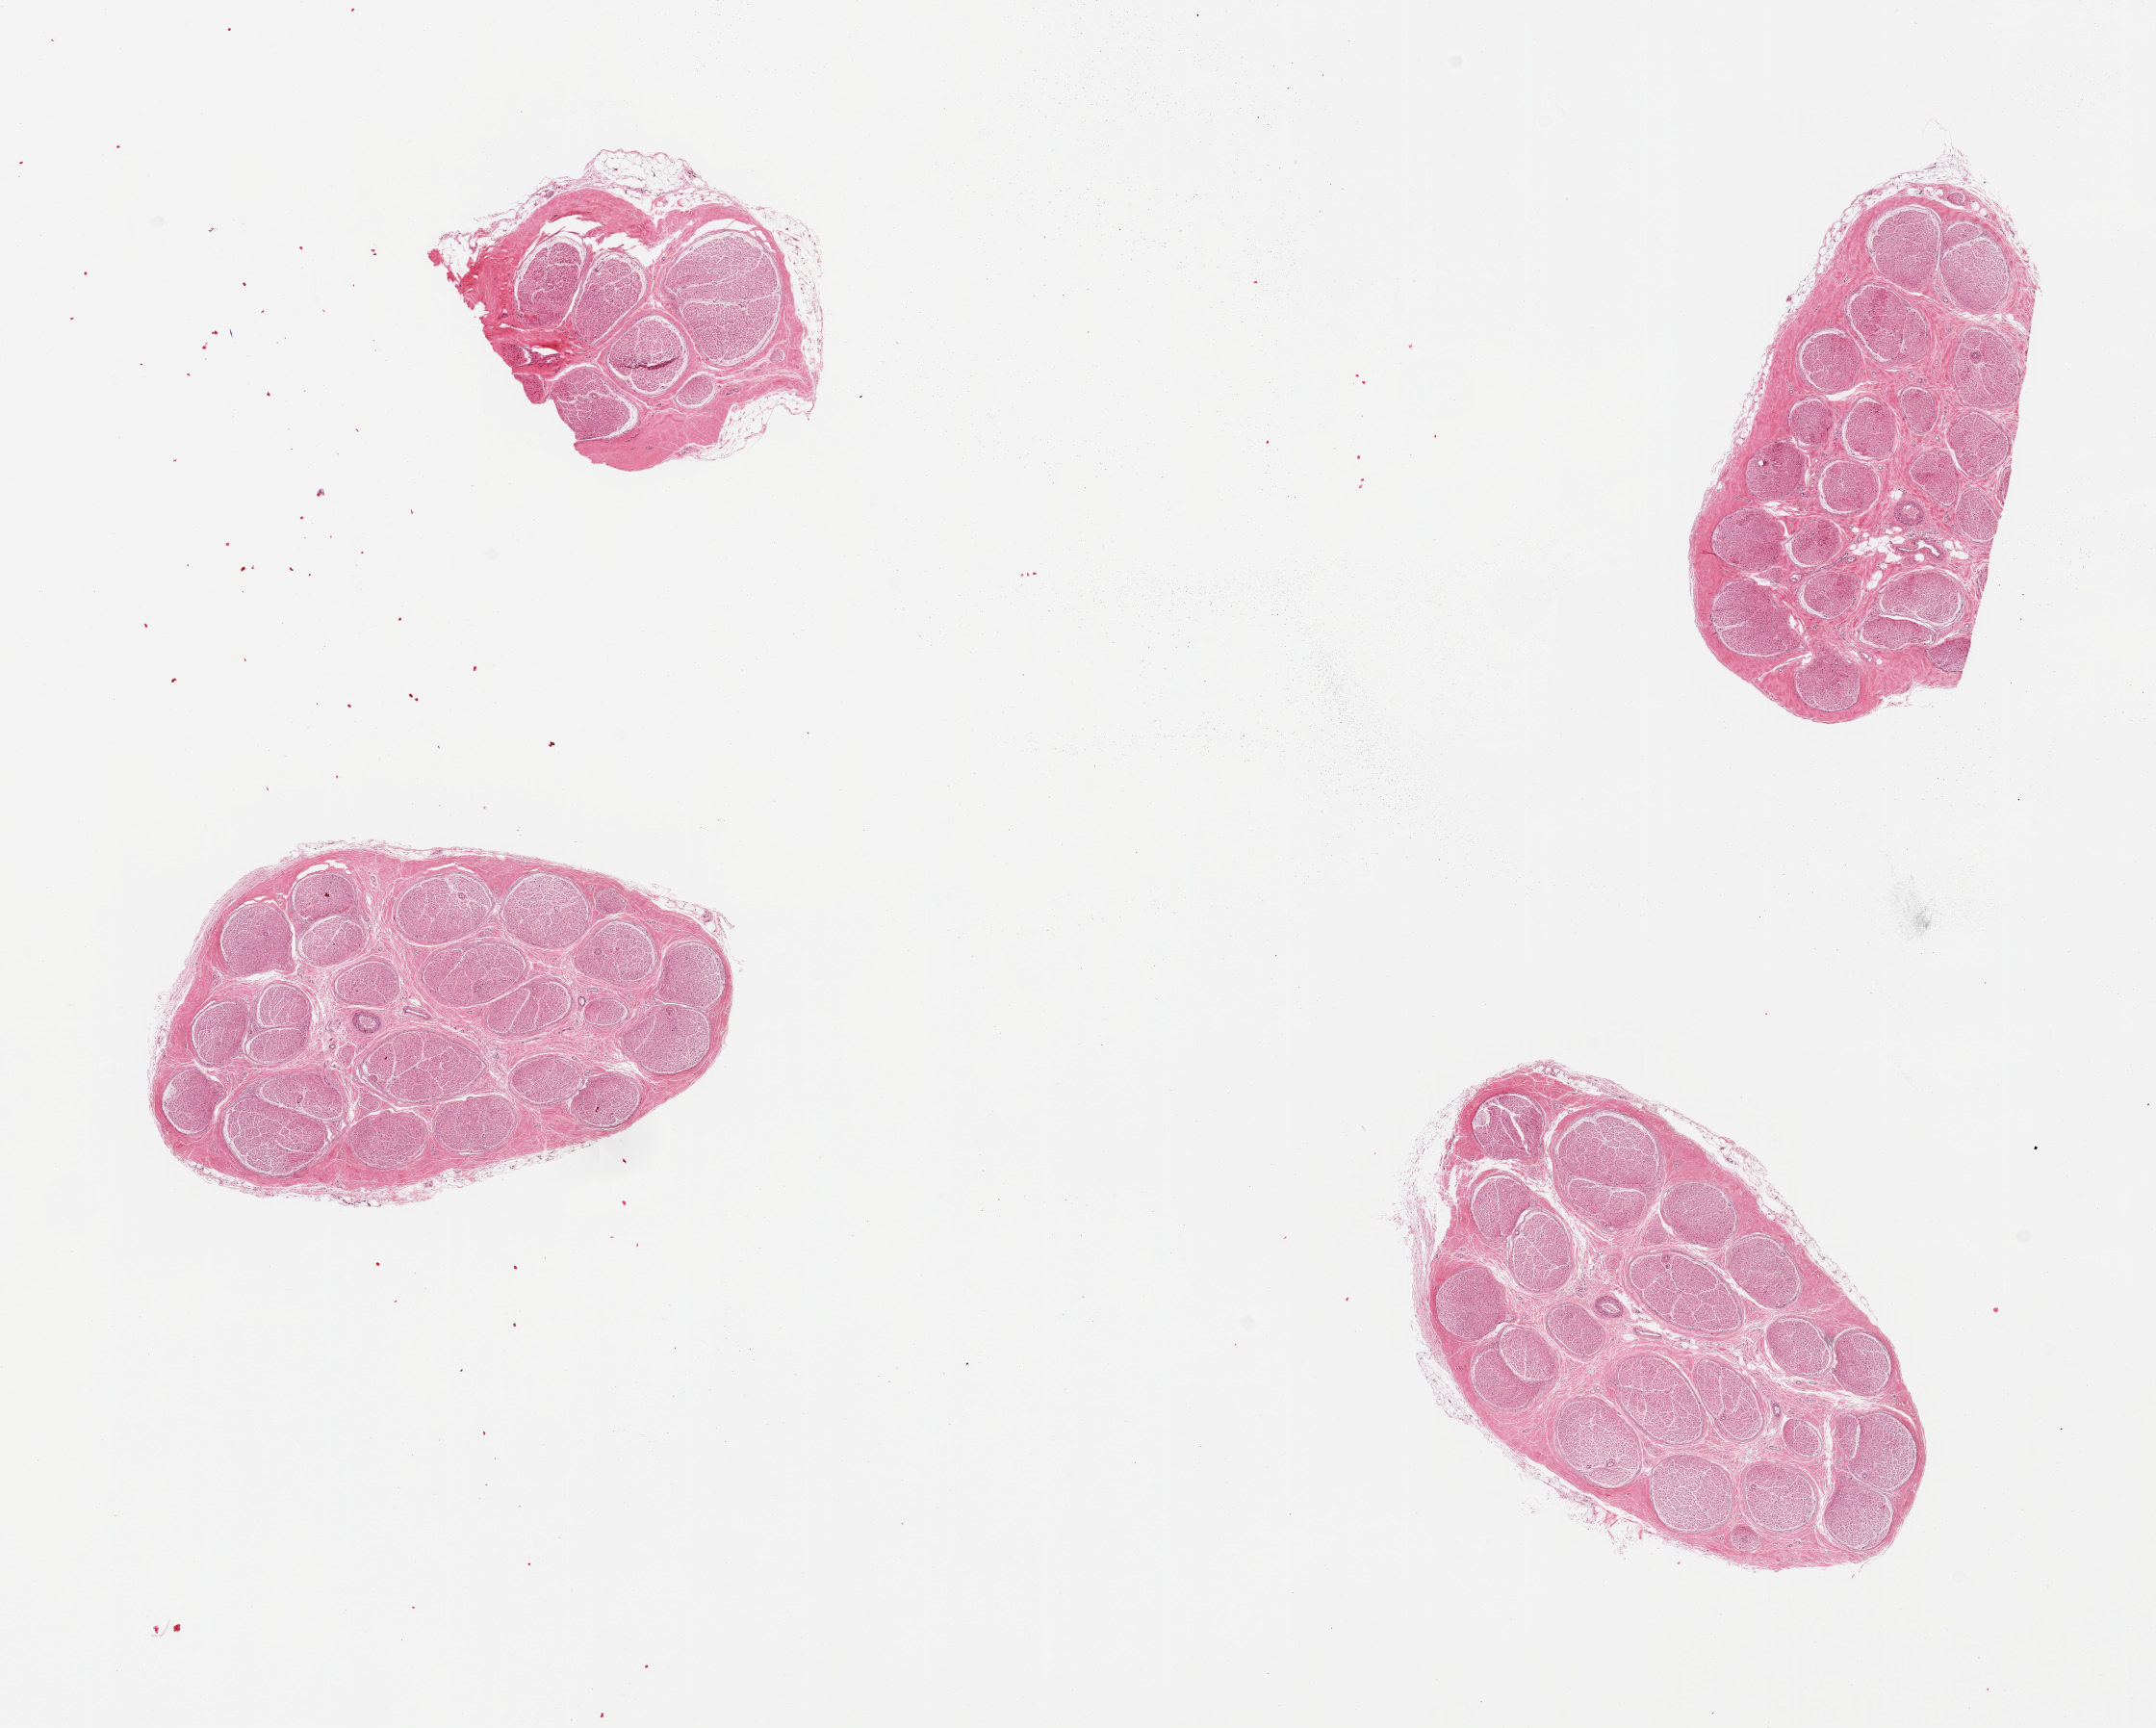
H&E whole-slide image, shown as a low-resolution overview of the whole scanned area (about 17.7 x 14.2 mm, from a 20x scan), PAXgene-fixed, paraffin-embedded tissue, section of tibial nerve (target tissue), tissue donor sample. Donor sex: male.
Pathologist's review note for this sample: 4 pieces; well trimmed.